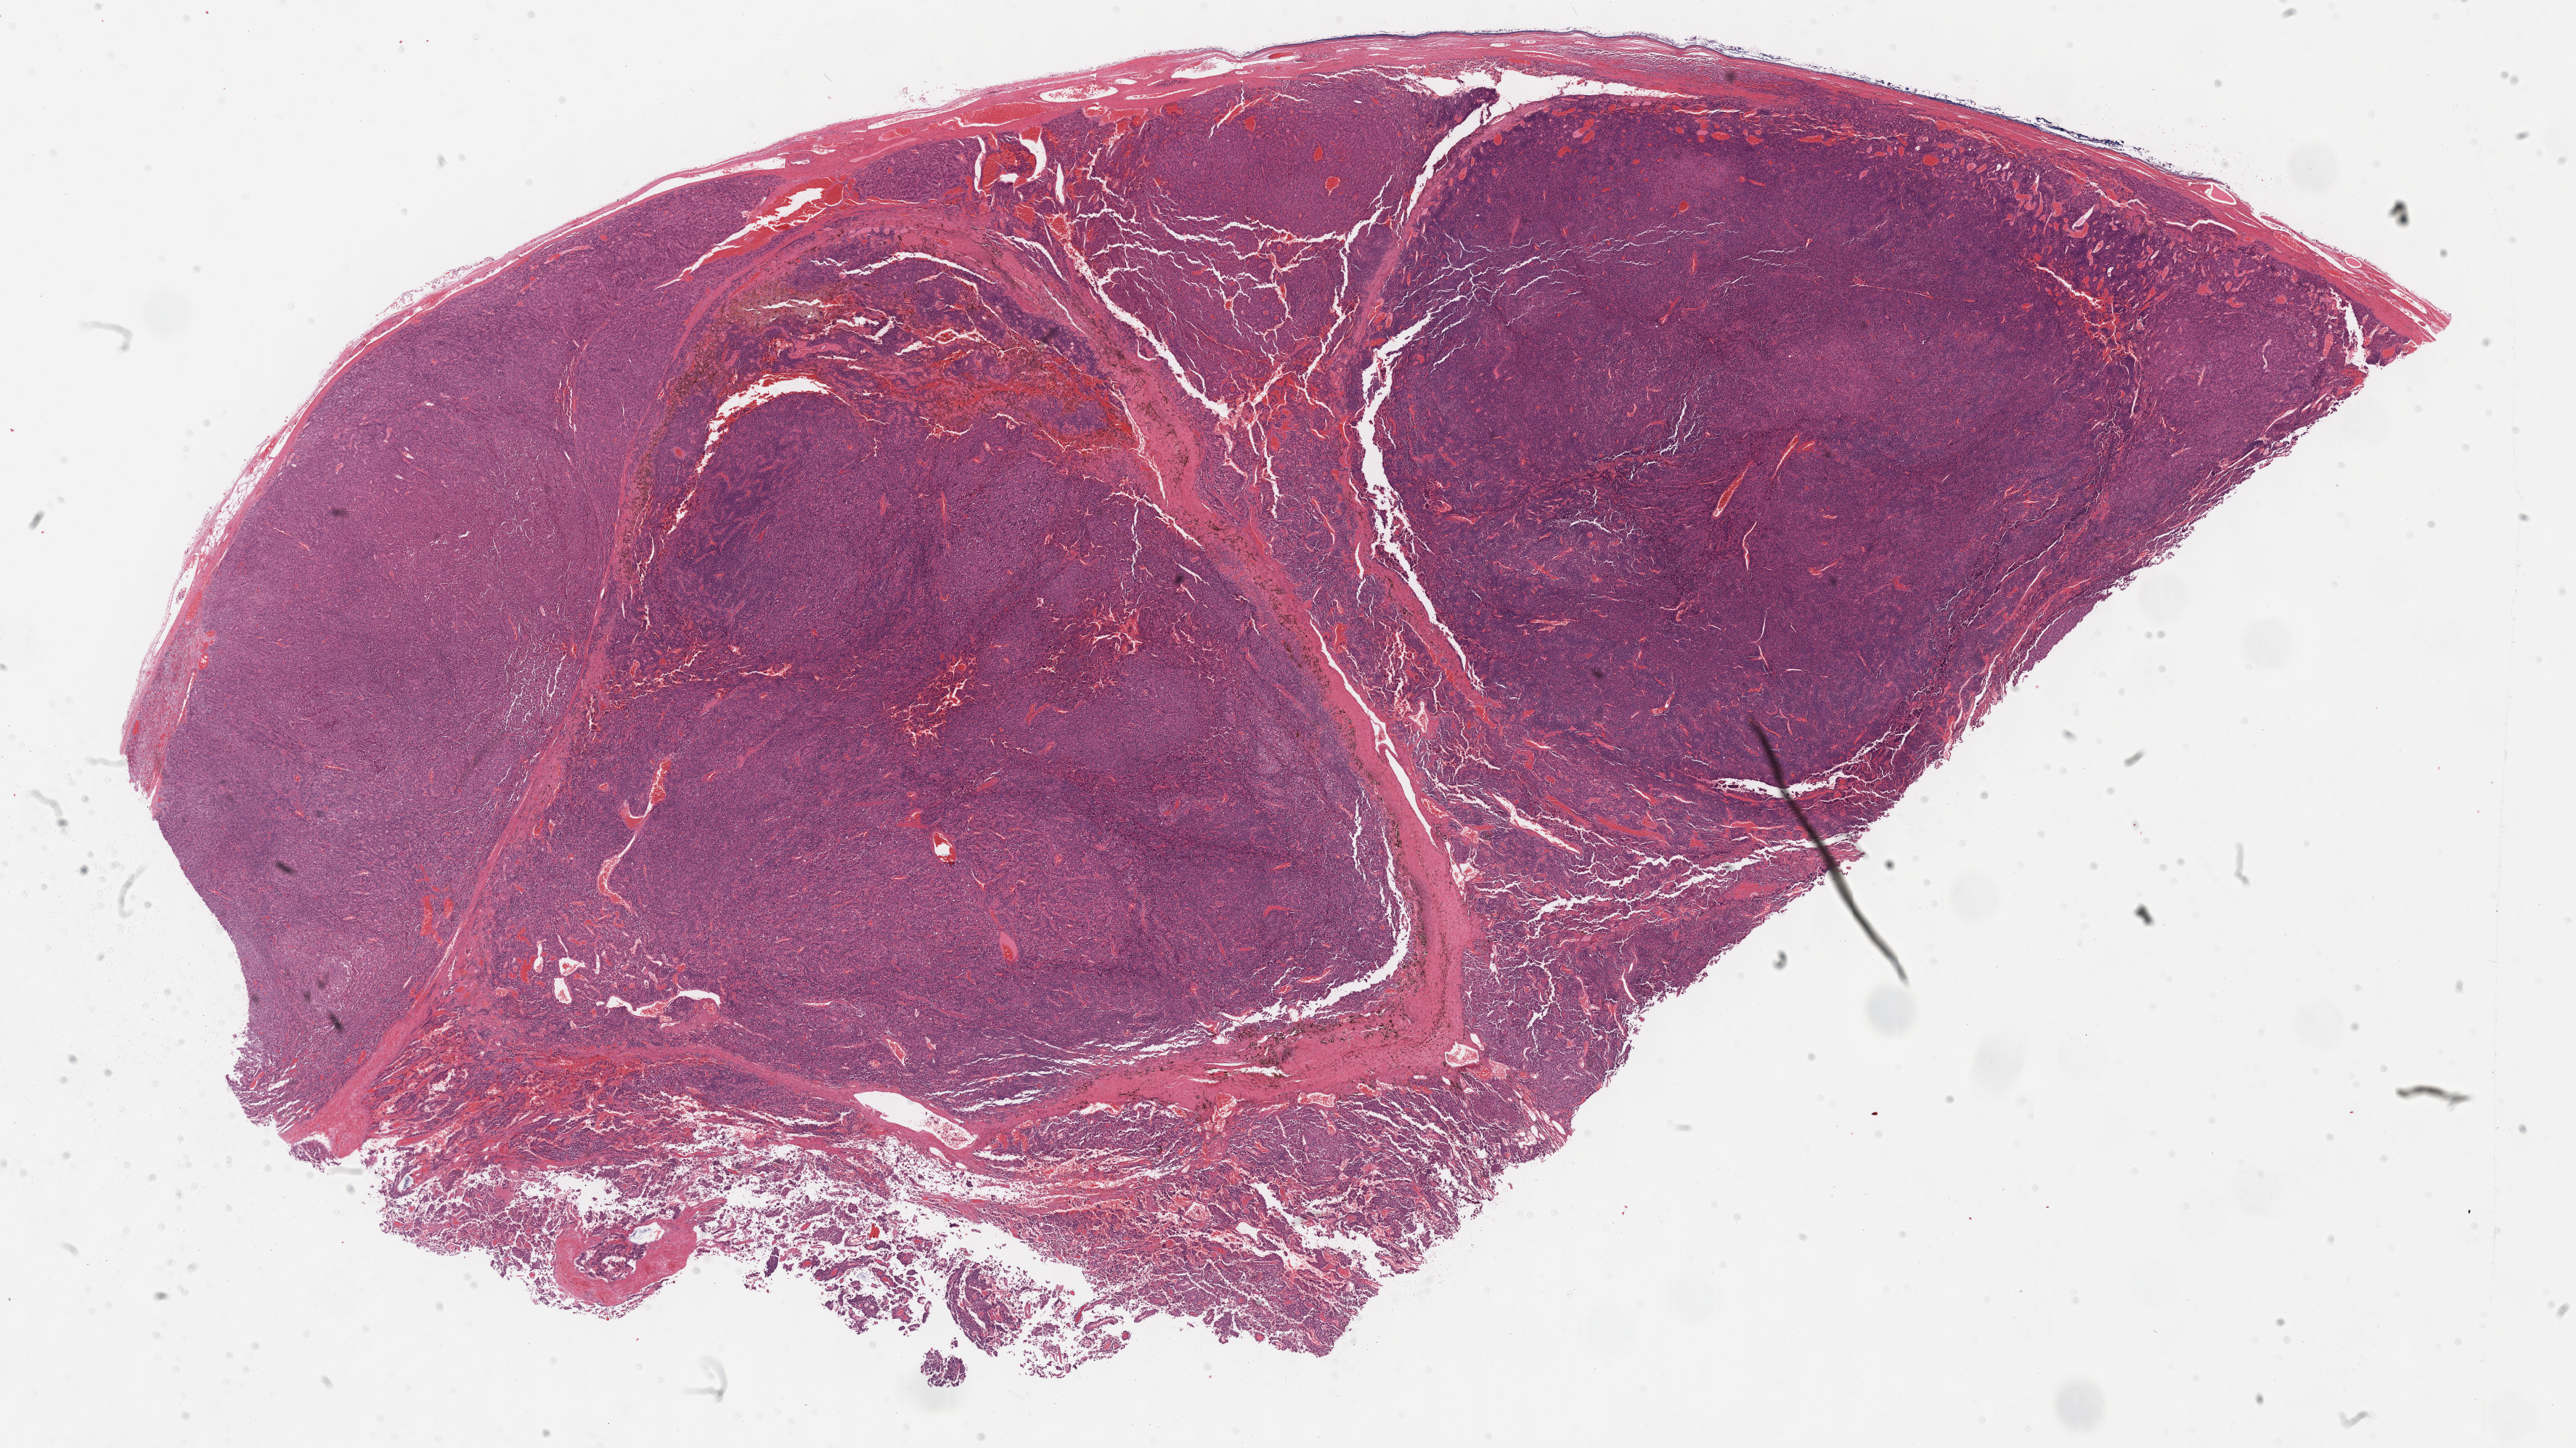
H&E whole-slide image, a low-resolution overview of the entire scanned area, about 28.7 x 16.1 mm (from a 40x scan). FFPE section. Primary tumour sample from the adrenal cortex. Male, age 58 years at initial diagnosis.
Pathologic diagnosis: Adrenal cortical carcinoma (cortex of adrenal gland).